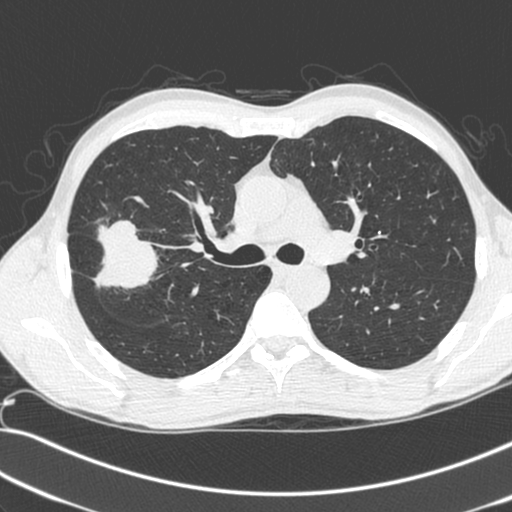
Chest CT (low-dose screening protocol), one axial image. Baseline screening round. Lung window (W 1500 / L -600 HU). 1.3 mm slice thickness. Standard (soft-tissue) reconstruction kernel (C). Slice 89 of 281 in the series. Male participant, aged 55 years at enrolment.
Expert reader's lesion annotation, bounding box [x1, y1, x2, y2] px = [68, 222, 156, 299]. Reader record for this screening exam (exam-level; its link to the box is not recorded): non-calcified nodule or mass ≥4 mm, right upper lobe, 52 × 39 mm, spiculated (stellate) margins, soft tissue attenuation.